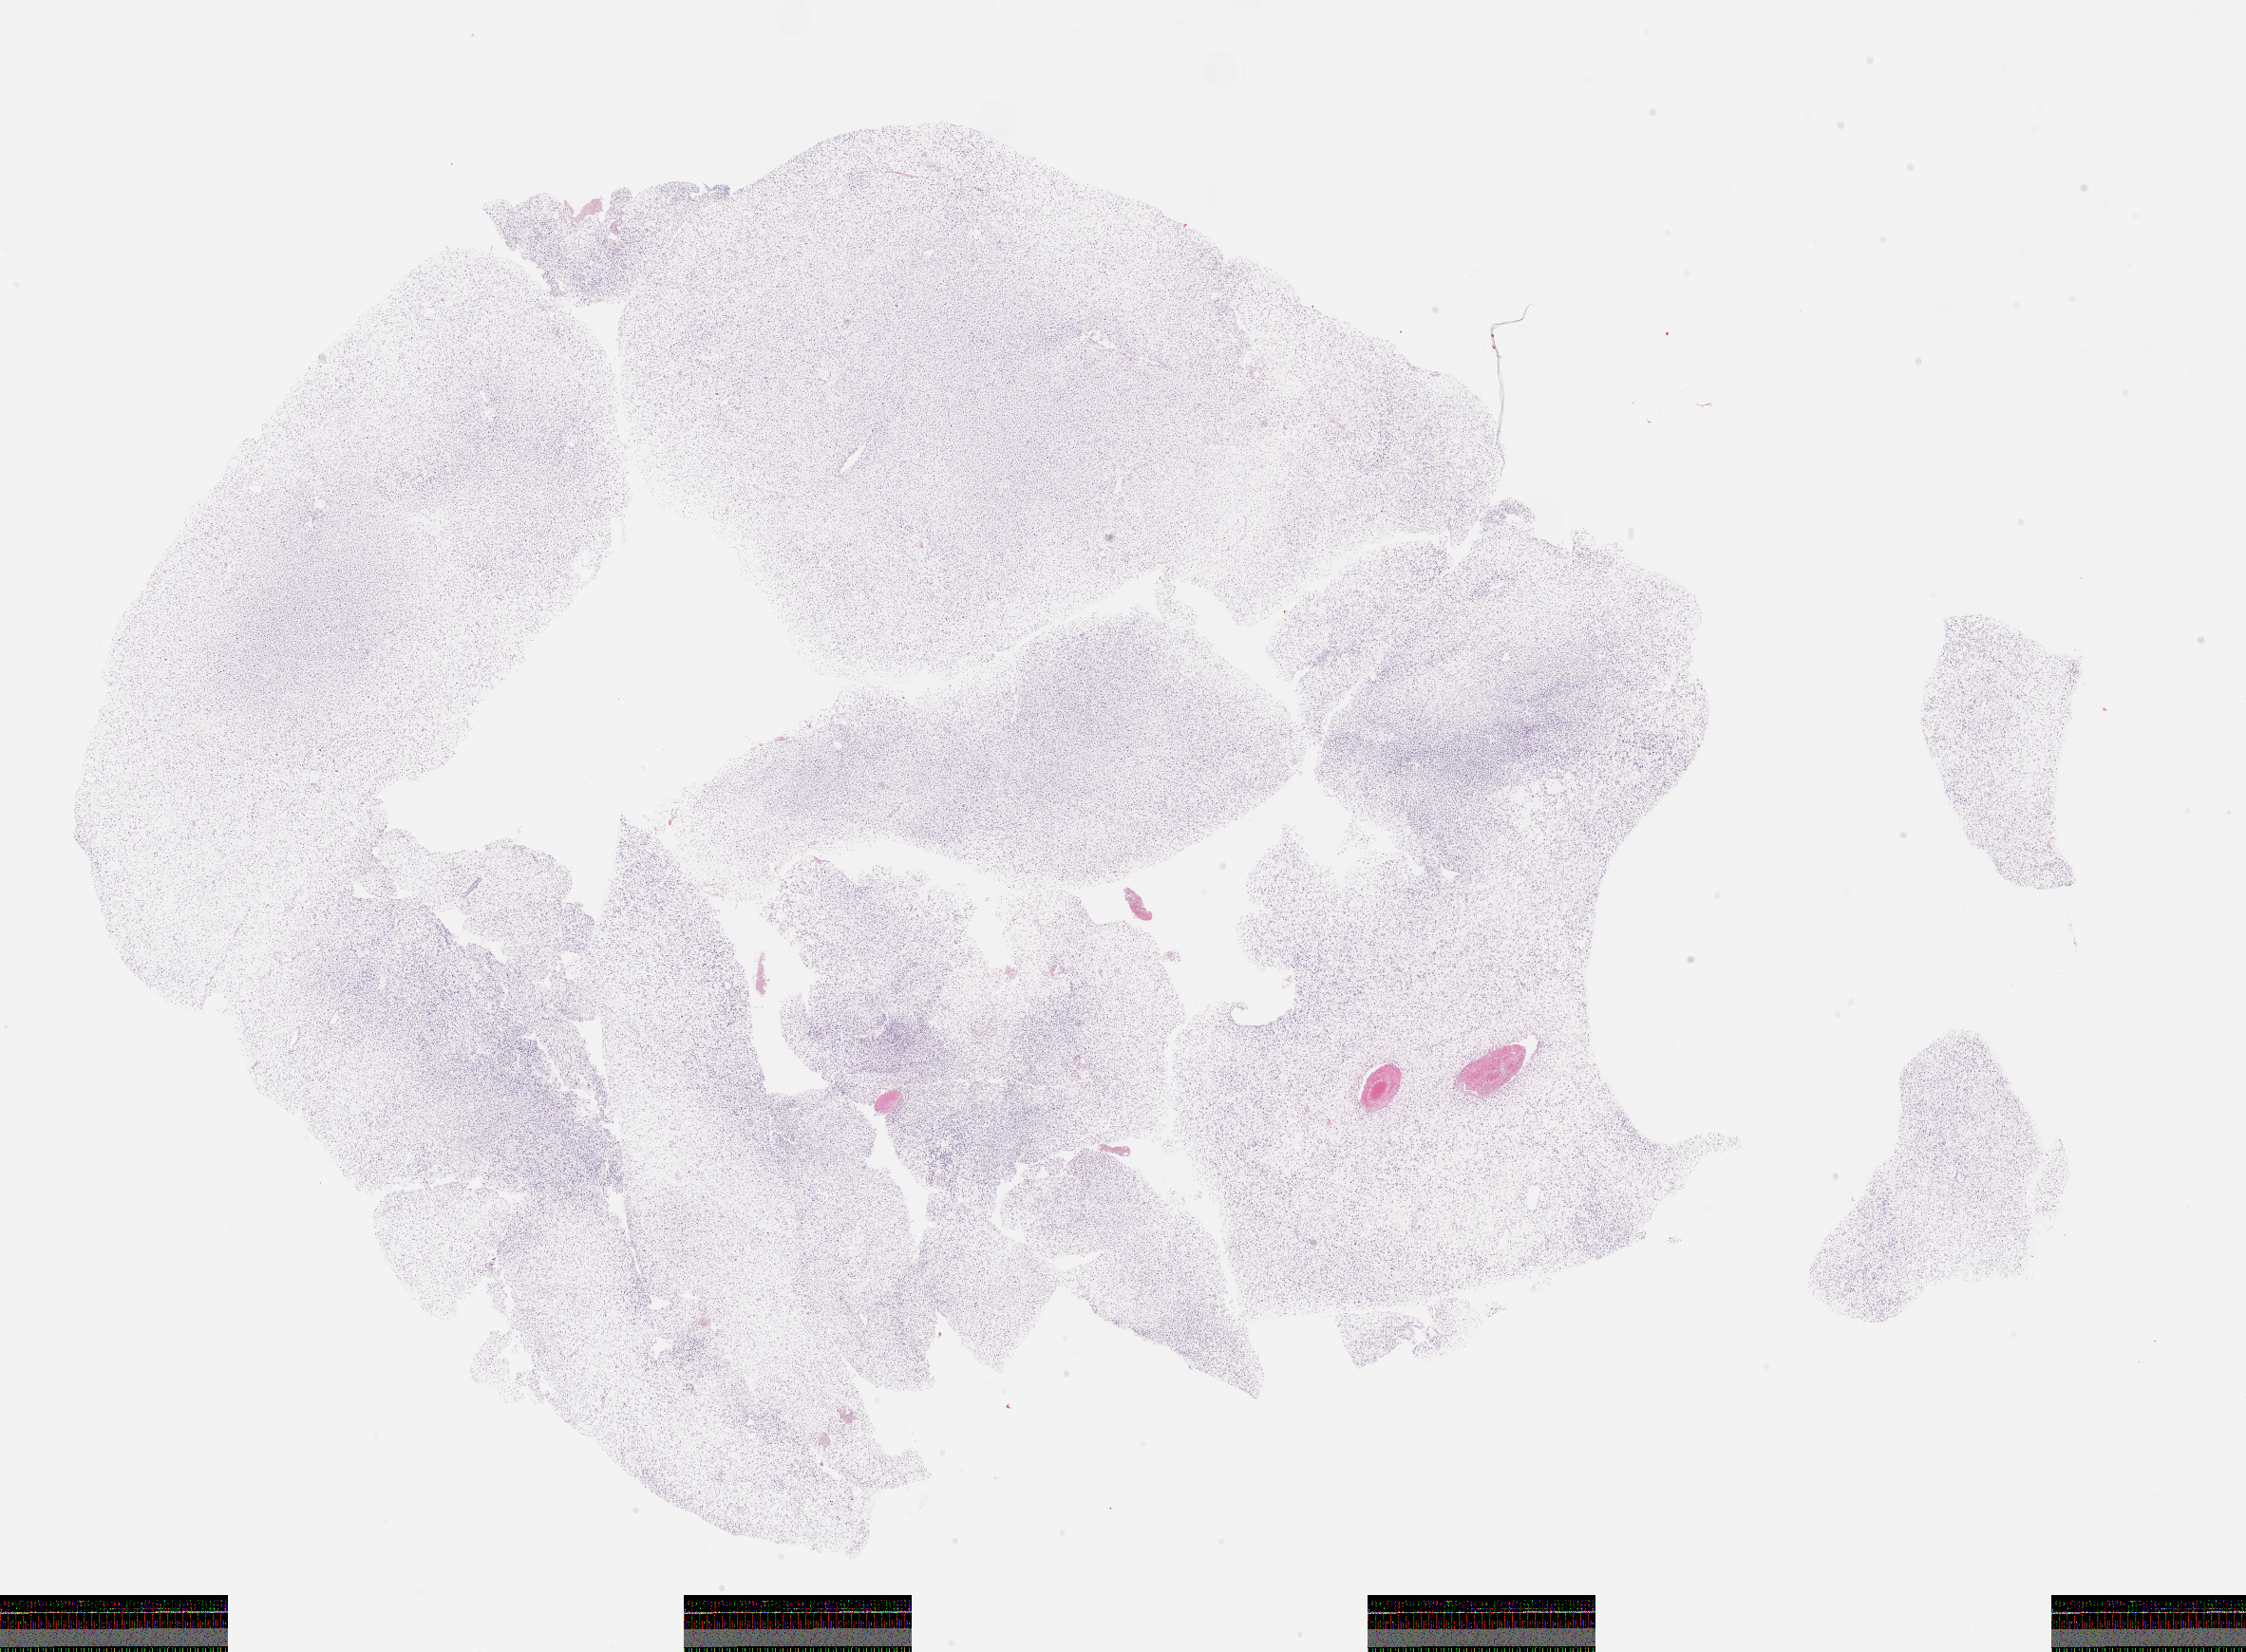
Whole-slide image, haematoxylin and eosin stain of tumor tissue, low-resolution overview of the scanned area, about 19.1 x 14.1 mm, formalin-fixed paraffin-embedded section, sample anatomic site: soft tissue, face/head (parapharyngeal pterygoid, right). Patient: male, age 10.8 years at diagnosis.
Metastatic status at presentation (as recorded): non-metastatic (unconfirmed). Primary site (case record): oropharynx. Stage (as recorded): 1. Diagnosis: rhabdomyosarcoma; histological classification: embryonal rhabdomyosarcoma.